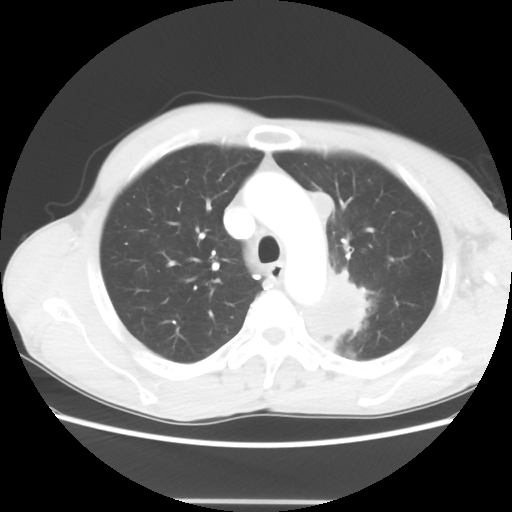
Chest CT, one axial slice; slice 48 of 62 in the series (ordered by position); reconstruction kernel STANDARD; 100 kVp; lung window (W 1500 / L -600 HU); 5 mm slice thickness; 512 × 512 image matrix, field of view 360 × 360 mm. Patient: male, 61 years. From the clinical record (not read from this slice): clinical TNM (as recorded): T3 N1 M1.
Annotated regions visible in this slice (rectangle marked by the reading radiologist):
- lung tumour (recorded histology: adenocarcinoma): bounding box <293,265,369,352> (left, top, right, bottom; pixels)
- lung tumour (recorded histology: adenocarcinoma): <310,190,338,218>